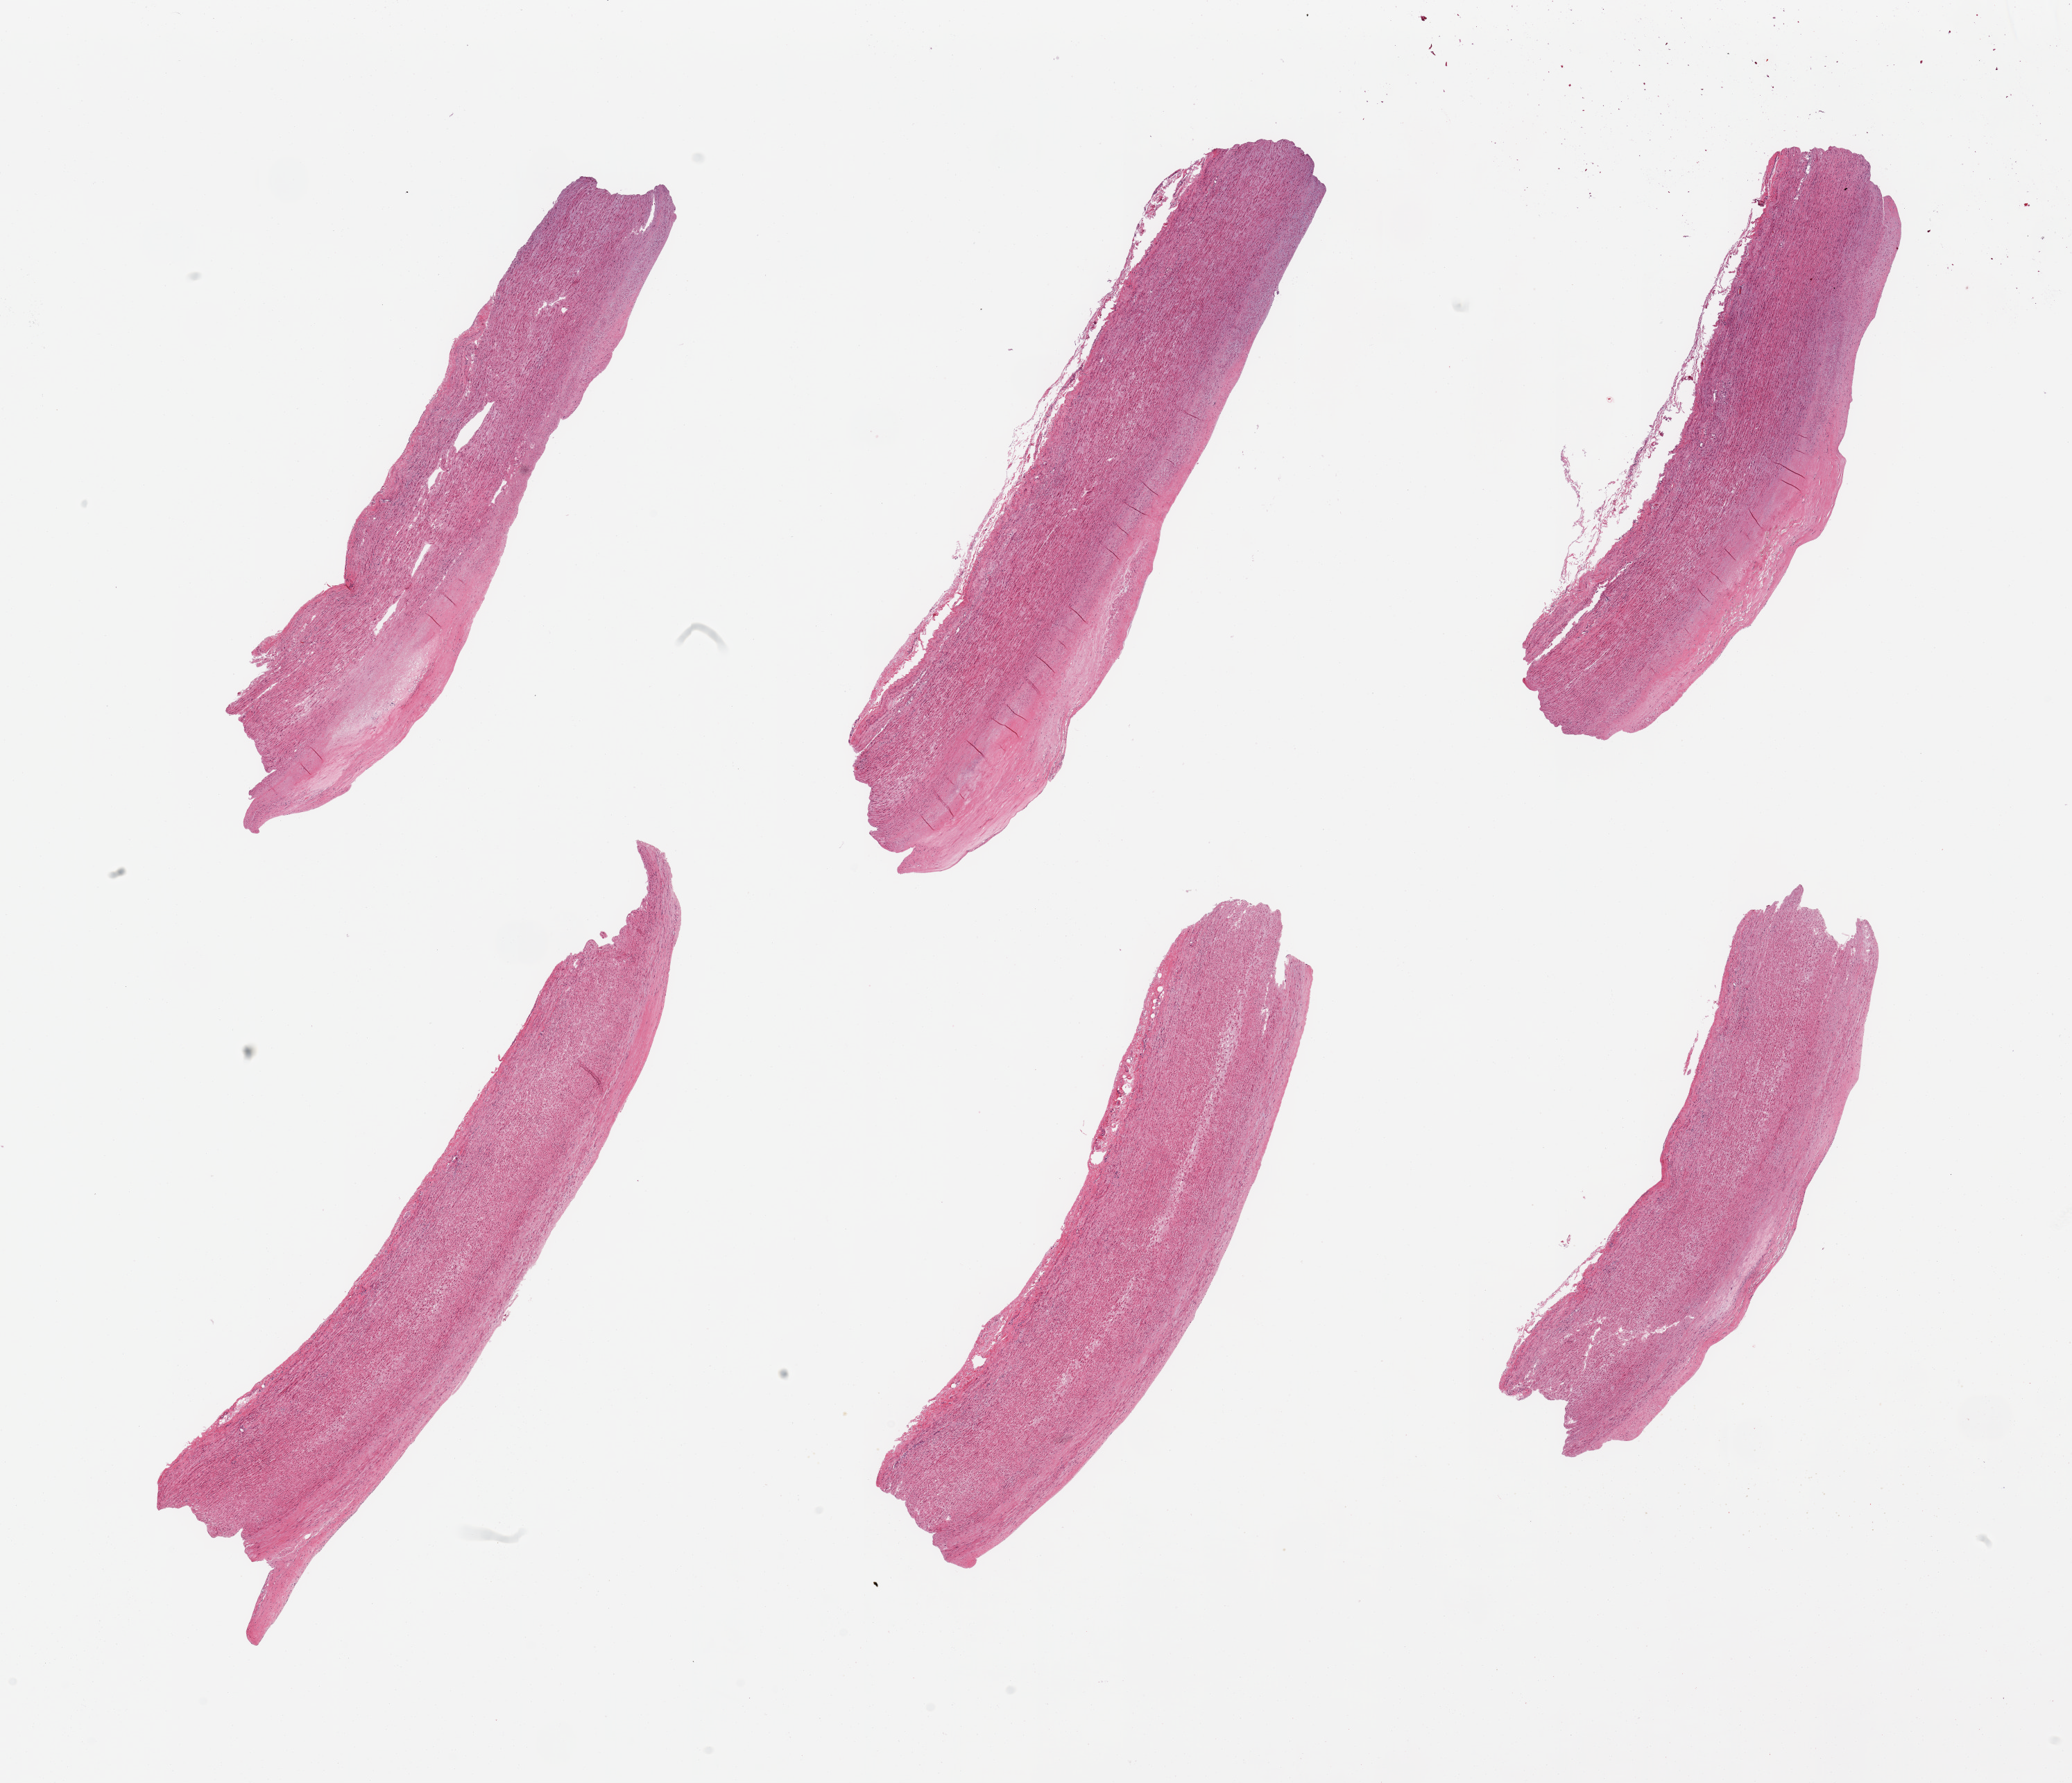
H&E whole-slide image, whole scanned area (about 23.6 x 20.3 mm) shown as a low-resolution overview; PAXgene-fixed paraffin-embedded (PFPE) section; sampled site (target tissue): aorta; donor tissue sample.
Review note (as recorded): 2 pieces, atherosis up to ~0.7mm.